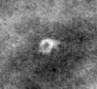
Region of interest cut from a scanned film mammogram (one marked finding); right breast; CC view.
- Finding: calcifications, morphology round and regular / lucent center; BI-RADS assessment category 2; benign; no additional work-up was recommended (benign without callback).